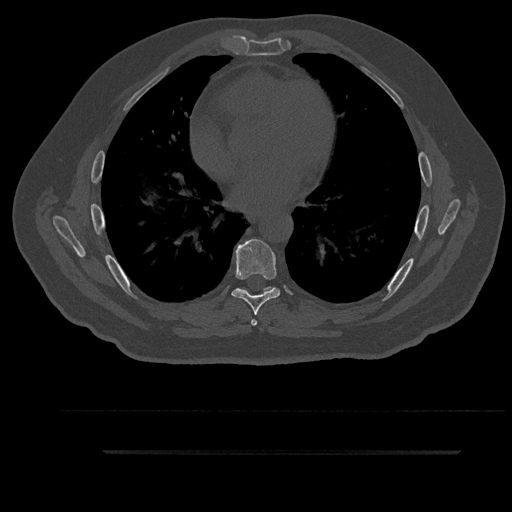
CT including the spine, one axial slice. Position 521 of 797 along the scan axis. Reconstruction kernel Br40s/3. Bone window (W 1800 / L 400 HU). 0.5 mm slice thickness. 512 × 512 image matrix. Male patient, age 63 years. From the clinical record (not read from this slice): primary cancer: renal.
Structures marked on this image (semi-automatic segmentation, software-assisted and operator-edited):
- T6 vertebra: bounding box [x1, y1, x2, y2] px = [241, 287, 274, 326]
- T7 vertebra: [231, 239, 281, 315]
- T8 vertebra: [241, 286, 272, 291]